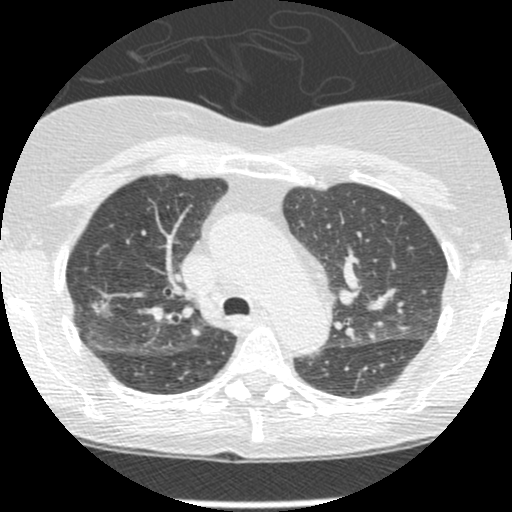
Low-dose screening chest CT, one axial slice. Slice 175 of 238 in the series (ordered by position). Reconstruction kernel STANDARD. 120 kVp. Lung window (W 1500 / L -600 HU). 1.25 mm slice thickness. 512 × 512 image matrix, field of view 288 × 288 mm.
Annotated regions visible in this slice (manually delineated by an expert):
- lesion 1 (tumor, upper lobe of right lung): bounding box [x1, y1, x2, y2] px = [93, 301, 110, 315]